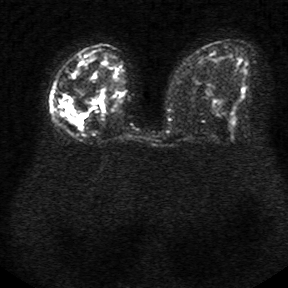
Breast MRI, one axial slice; slice 14 of 34 in the series (ordered by position); diffusion-weighted series; image 2 of 4 stored at this slice position (different b-values; order by instance number); 1.5 T; 5 mm slice thickness; 288 × 288 image matrix, field of view 340 × 340 mm. Female patient.
Structures marked on this image (expert manual segmentation):
- tumour on diffusion-weighted imaging: box from (x=60, y=89) to (x=107, y=131) px